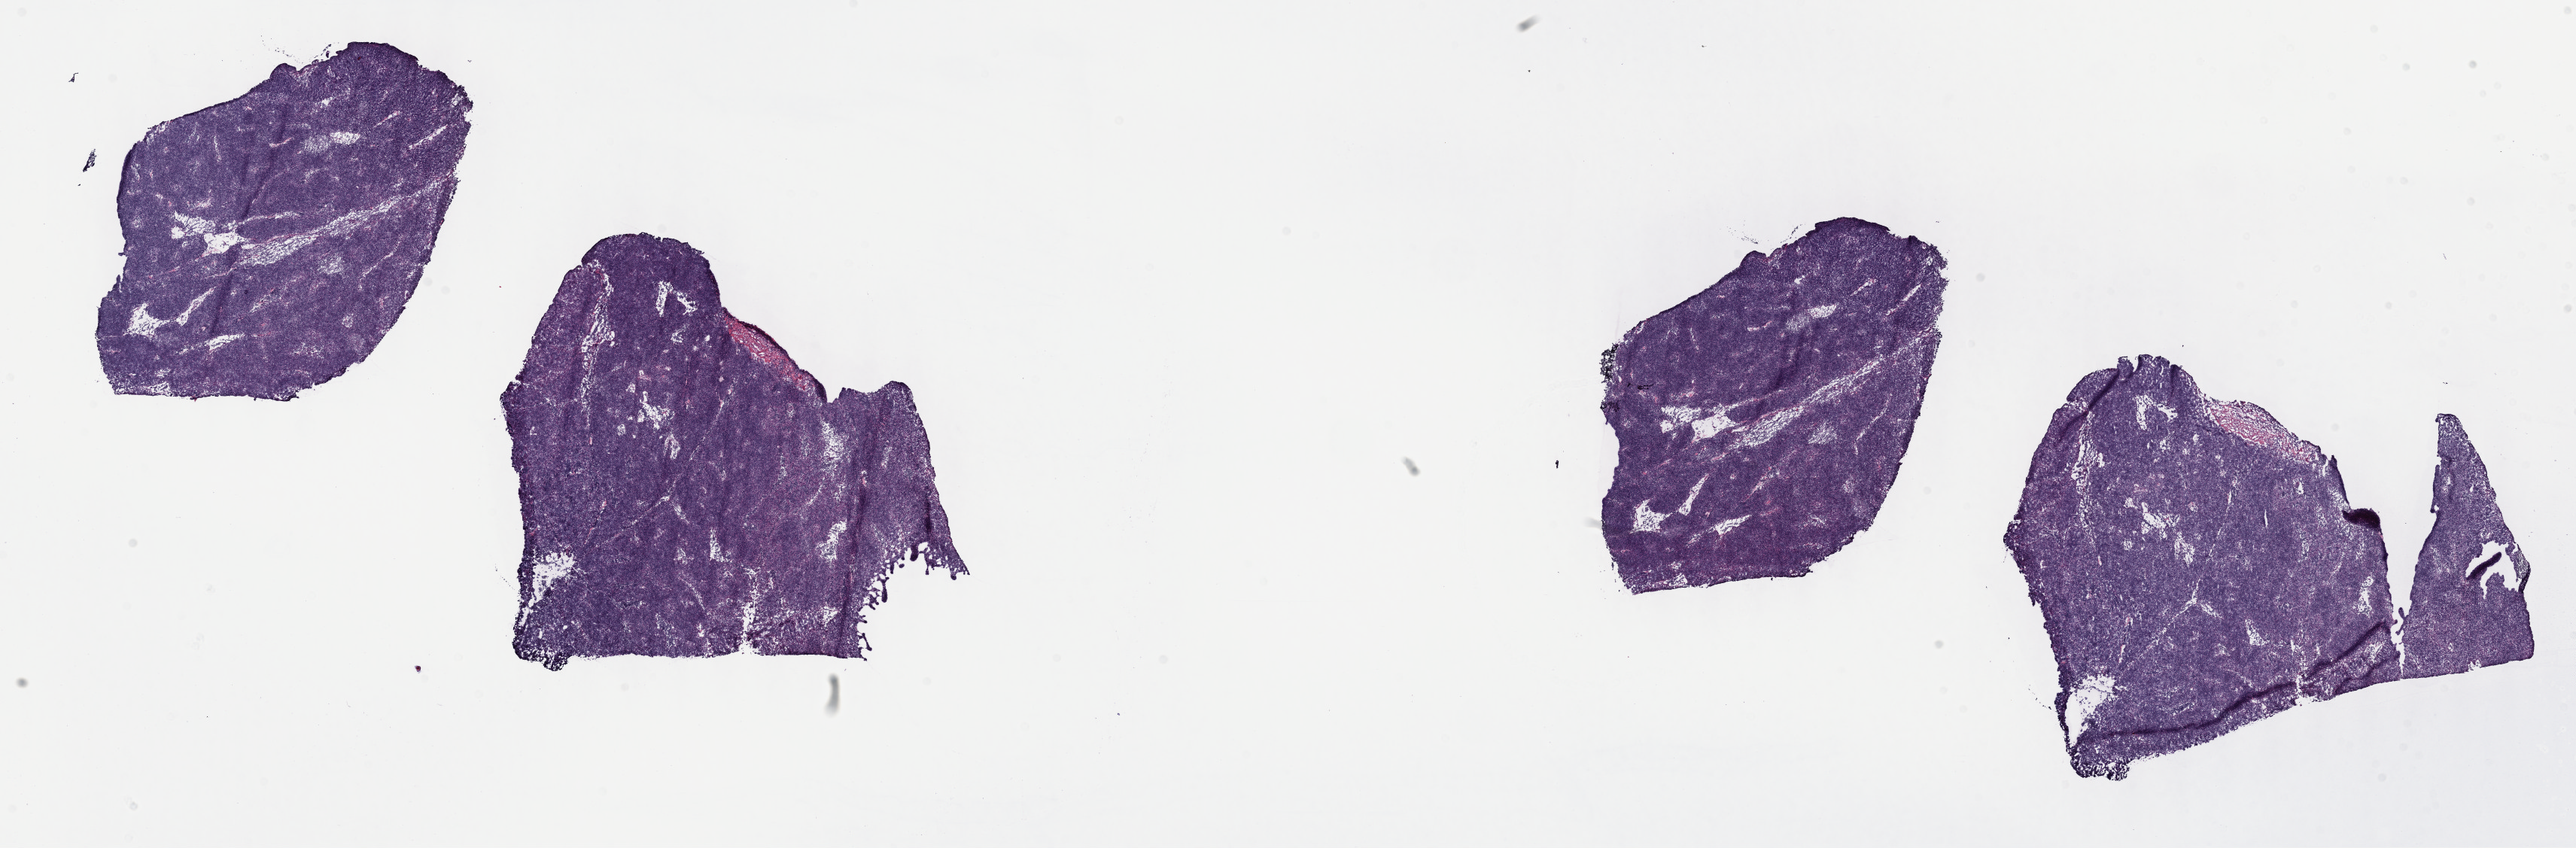
H&E whole-slide image, a low-resolution overview of the entire scanned area, about 27.7 x 9.1 mm (from a 40x scan). Frozen section from the top of the tissue portion. Sample: primary tumour, thymus. Female patient; age at initial diagnosis 44 years. Pathologist review of this section (percent, as recorded): tumour cells 85%, tumour nuclei 85%, normal cells 0%, stromal cells 15%, necrosis 0%. Inflammatory infiltration, as recorded: lymphocyte infiltration 3%, monocyte infiltration 1%, neutrophil infiltration 1%.
• pathologic diagnosis: Thymoma, type B2, malignant